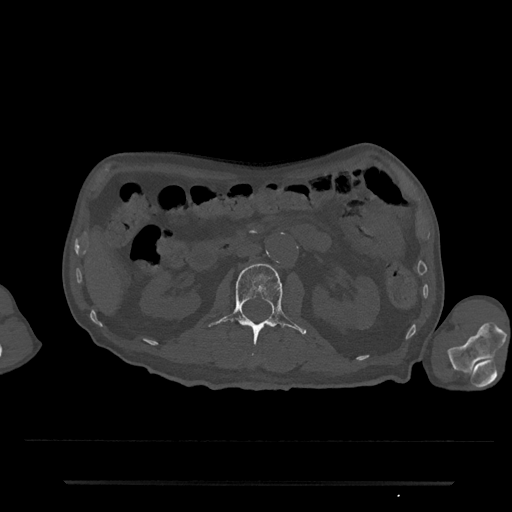
CT including the spine, one axial slice; position 66 of 797 along the scan axis; bone window (W 1800 / L 400 HU); 0.5 mm slice thickness; 512 × 512 image matrix, field of view 427 × 427 mm. Patient: male, 74 years. Case-level facts recorded for this patient, not image findings: primary cancer: prostate.
Structures marked on this image (semi-automatic segmentation, software-assisted and operator-edited):
- L2 vertebra: bounding box <209,263,307,343> (left, top, right, bottom; pixels)